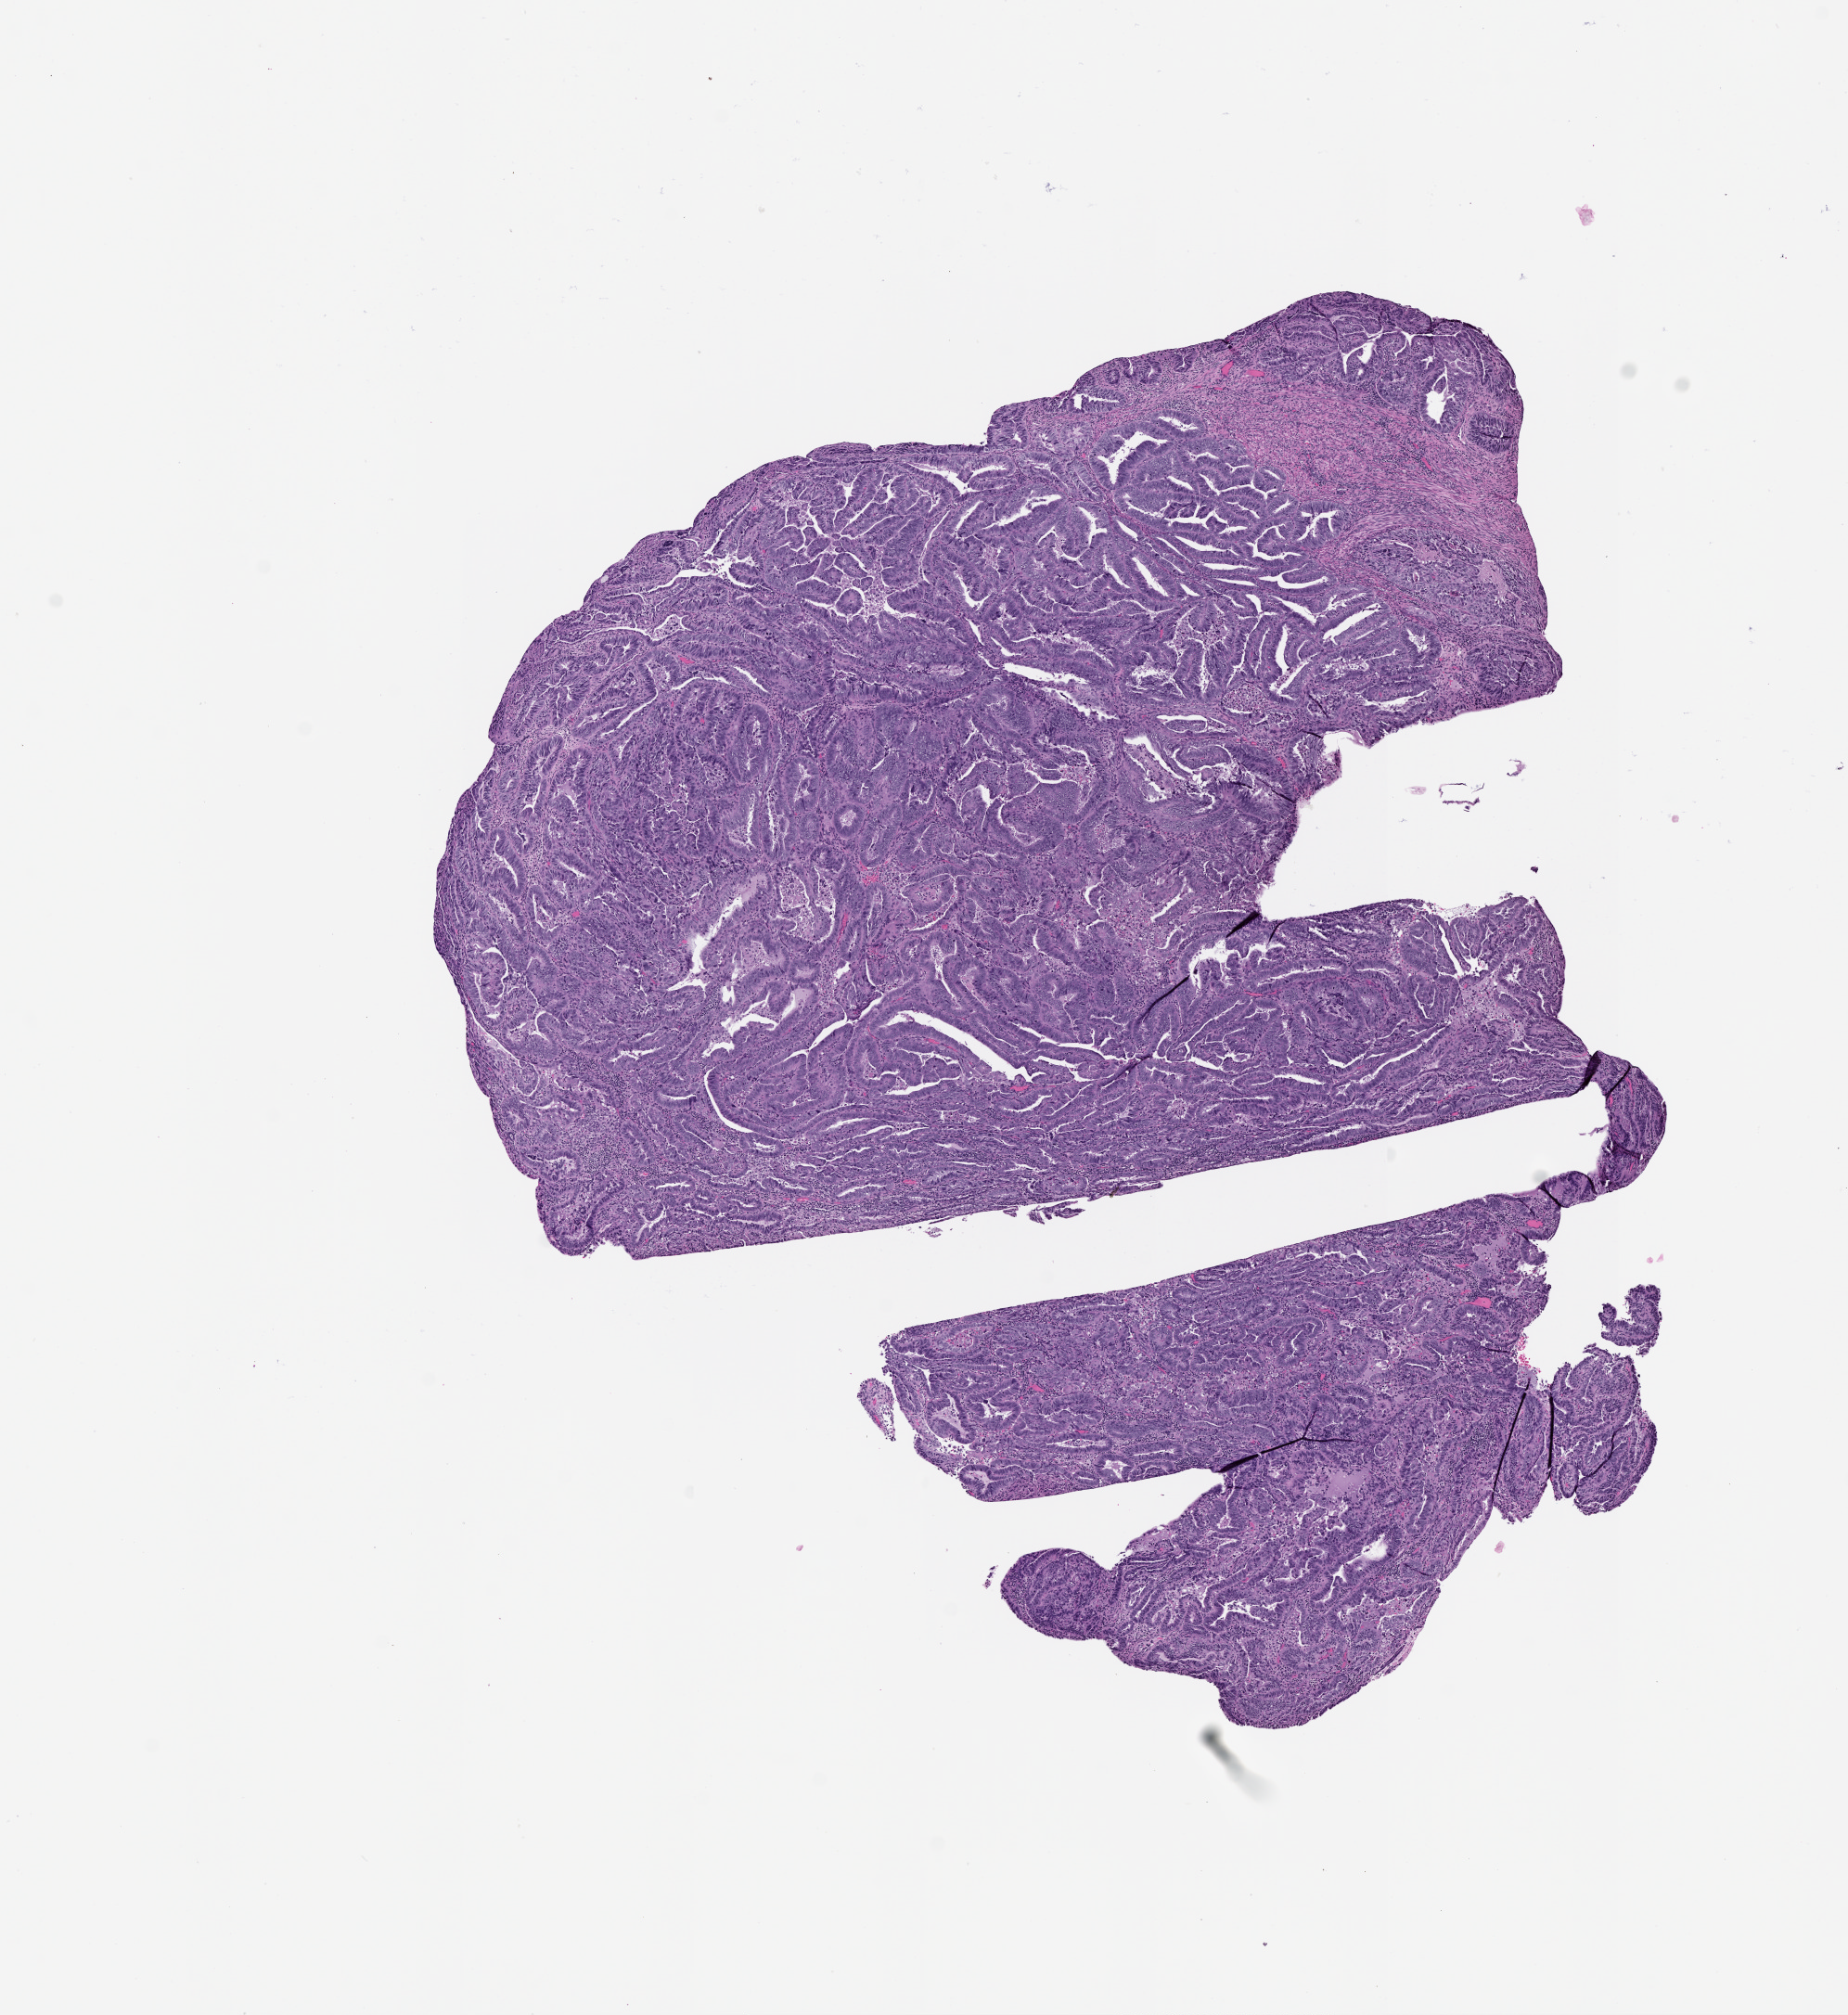
Hematoxylin and eosin (H&E) stained whole-slide image — shown as a low-resolution overview of the whole scanned area (about 8.0 x 8.7 mm, acquisition: 20x scan); tumour tissue sample, sampled site: uterus. Patient: female, age 58 years. Histologic grade: G3 (poorly differentiated). Slide review estimates, as recorded: tumour nuclei 80%, necrosis 0%.
- primary tumour site (as recorded): posterior endometrium
- histologic diagnosis: Endometrioid adenocarcinoma, NOS
- AJCC pathologic stage: IIIC1